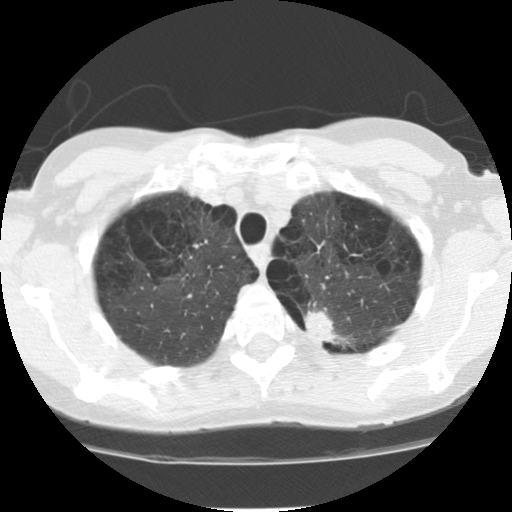
Low-dose screening chest CT, axial slice. Baseline annual screen. Lung window (W 1500 / L -600 HU). 2.5 mm slice thickness. Standard (soft-tissue) reconstruction kernel (STANDARD). Slice 21 of 116 in the series. 512 × 512 image matrix. Female participant, aged 61 years at enrolment. Current smoker at enrolment.
- Lesion marked by an expert reader, box from (x=289, y=300) to (x=347, y=354) px.
- The screening reader recorded 4 non-calcified nodules or masses ≥4 mm on this exam (left upper lobe, right lower lobe, right middle lobe, left lower lobe); which of them this box marks is not recorded.
- Official screen result: positive, change unspecified: nodule(s) >= 4 mm or enlarging nodule(s), mass(es), or other non-specific abnormalities suspicious for lung cancer.
- Lung cancer was diagnosed 68 days after this screen: adenocarcinoma, NOS, left upper lobe, poorly differentiated (G3), stage IB (AJCC 6th edition), 17 mm at pathology.